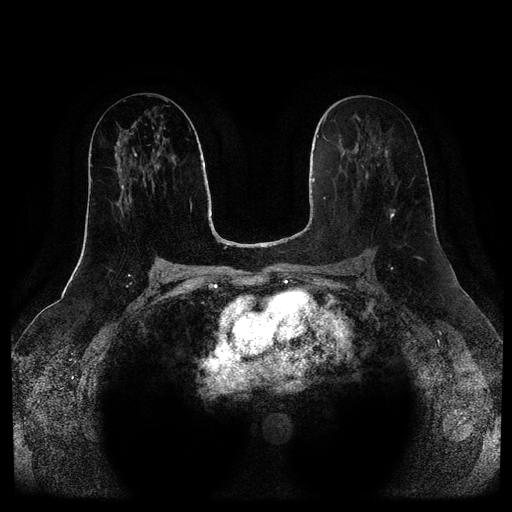
Breast MRI (dynamic contrast-enhanced, multi-phase), one axial slice; slice 46 of 116 in the series (ordered by position); dynamic contrast-enhanced series, time point 2 of 5 at this slice position (early post-contrast); 1.5 T; TE 2.6 ms, TR 5.2 ms; 512 × 512 image matrix, field of view 380 × 380 mm. Patient: female, 57 years.
Annotated regions visible in this slice (semi-automatic segmentation, software-assisted and operator-edited):
- breast lesion (labelled 'tumour' in the annotation; benign lesions carry a separate 'benign' label): box from (x=390, y=209) to (x=395, y=218) px